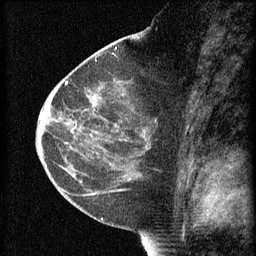
Breast MRI (dynamic contrast-enhanced), one sagittal slice. Slice 35 of 60 in the series (ordered by position). 3 images stored at this slice position (order not interpretable as contrast timing). 1.5 T. TE 4.2 ms, TR 8.2 ms. 2 mm slice thickness. 256 × 256 image matrix, field of view 180 × 180 mm. Female patient, age 44 years.
Outlined on this slice (semi-automatic segmentation, software-assisted and operator-edited):
- analysis volume of interest (the breast-tissue region the enhancement analysis was run in; not a lesion): bounding box <73,82,158,165> (left, top, right, bottom; pixels)
- tumour enhancement mask (voxels above the 70 % enhancement threshold inside the analysis volume of interest): <75,96,146,137>